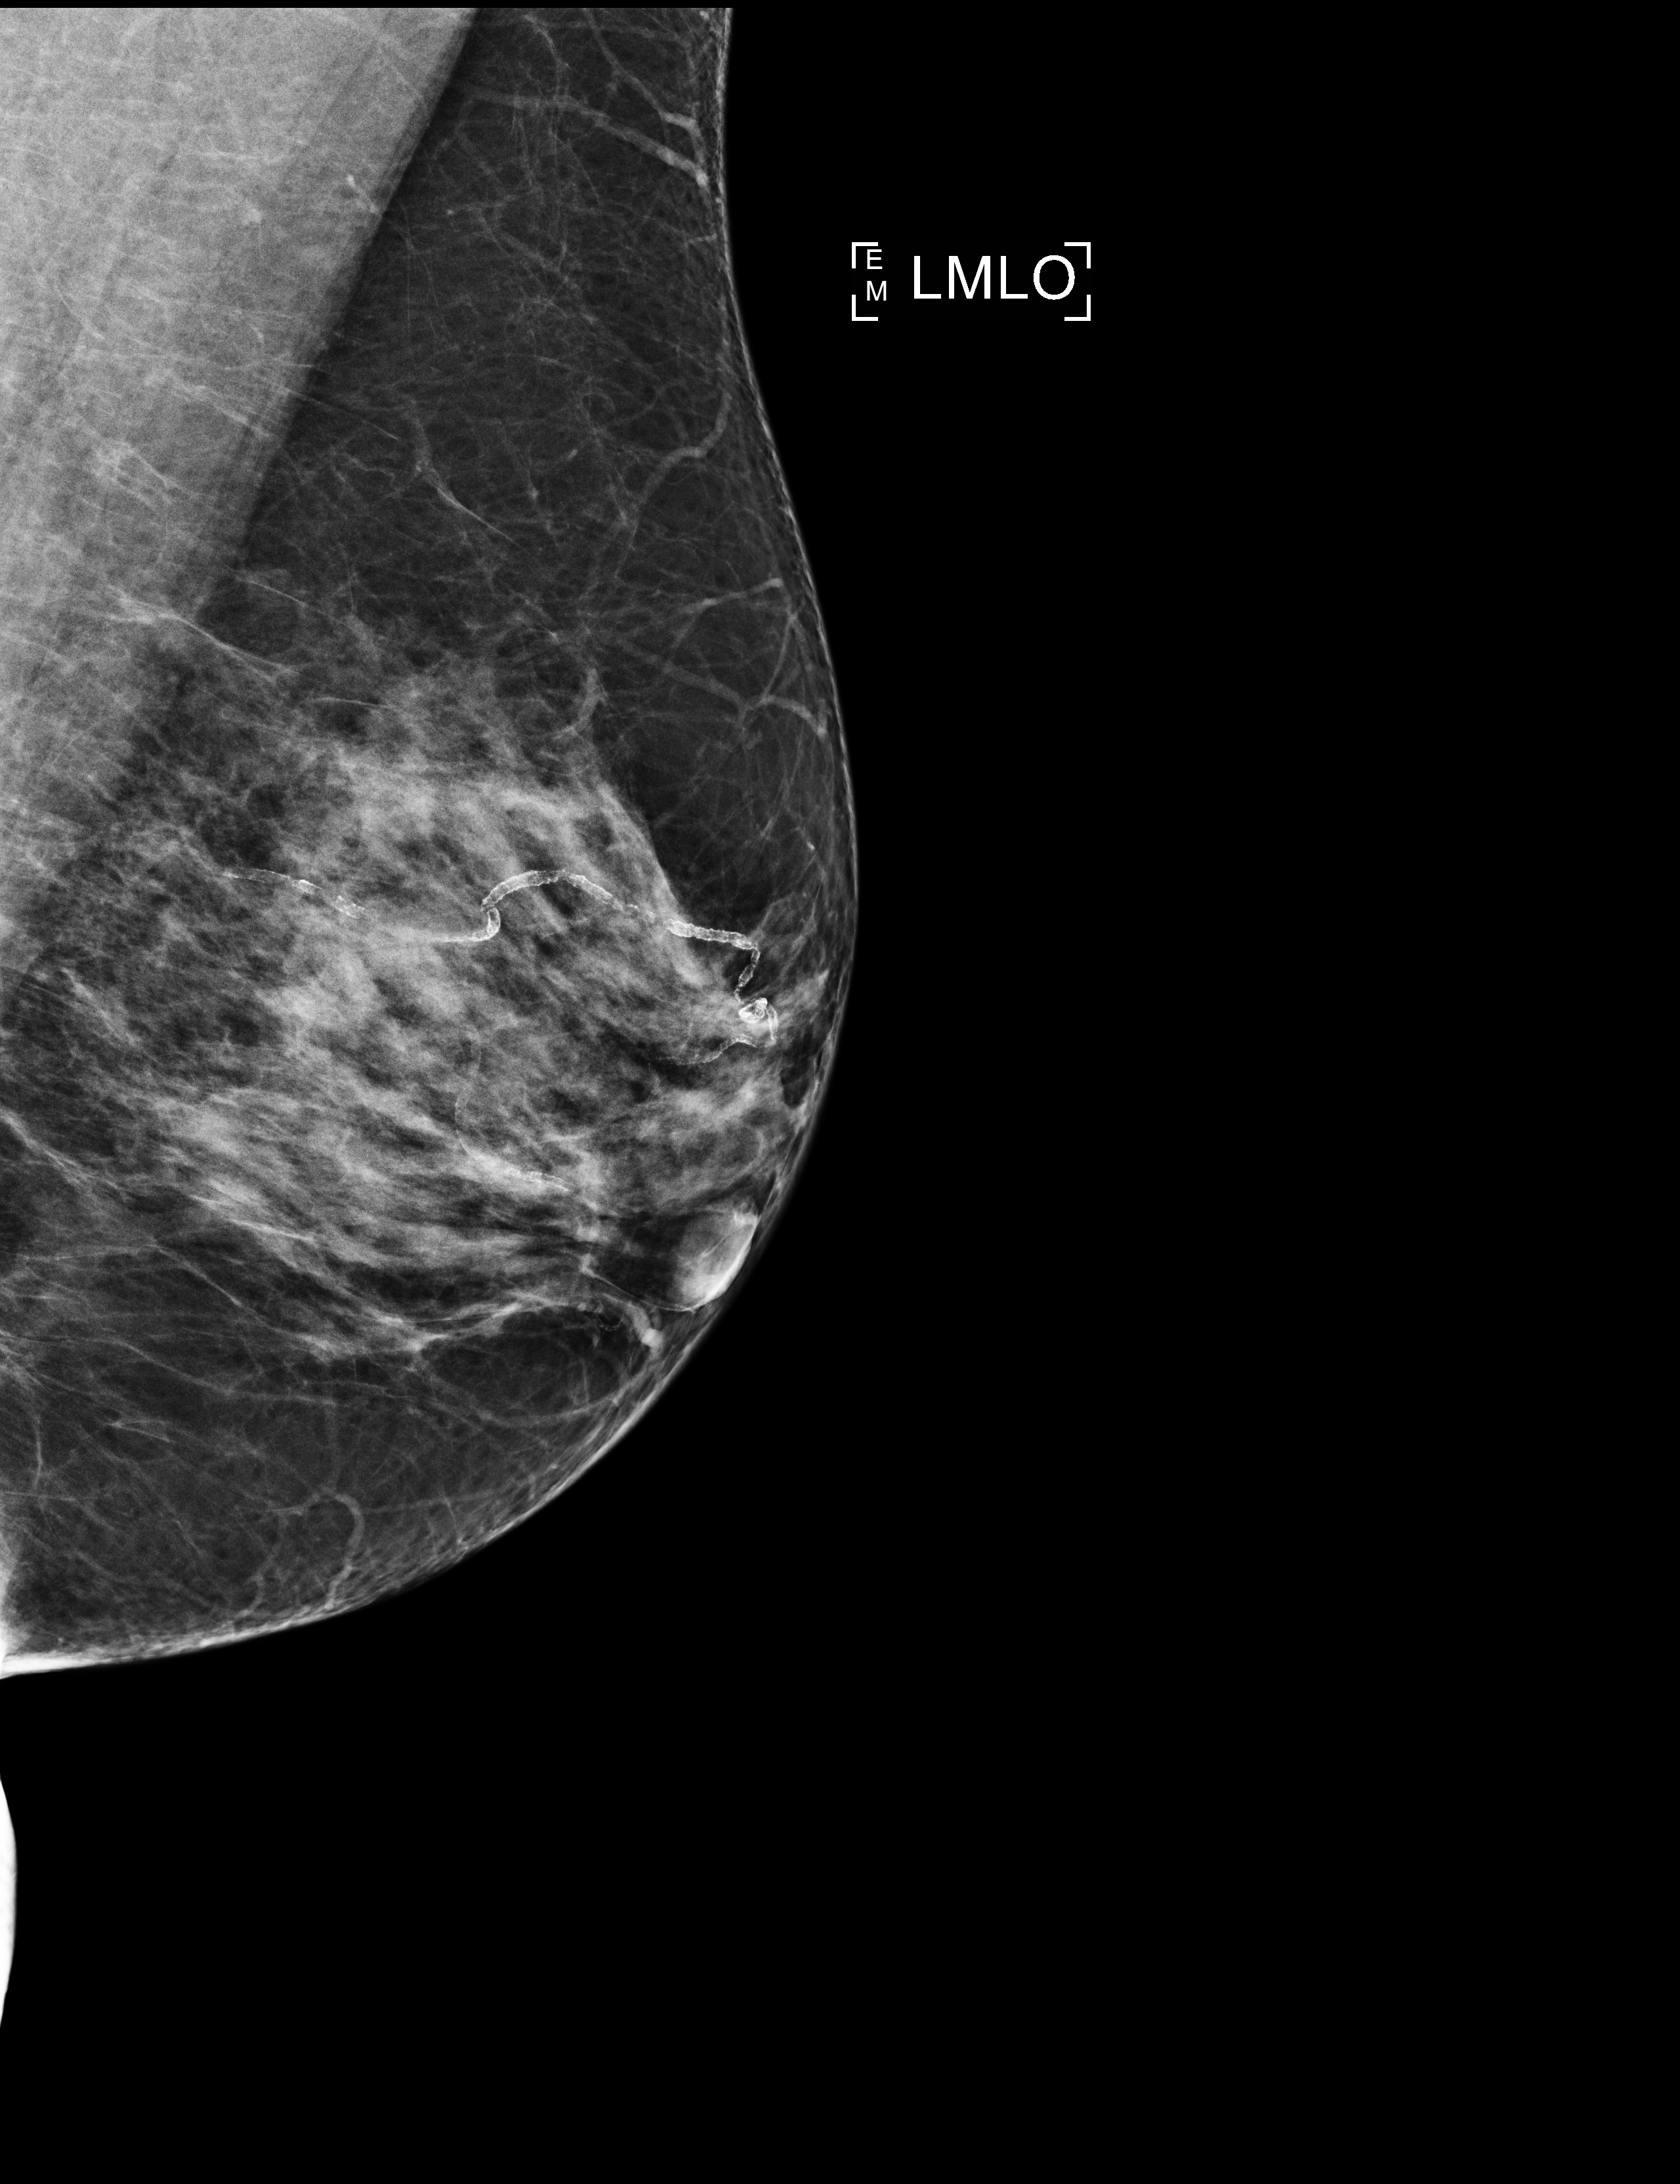
Digital mammogram (FFDM); left breast; MLO view; annual screening mammography examination; compressed breast thickness 60 mm. Female patient, age 59 years.
Final BI-RADS category for the screening round (tomosynthesis exam, both breasts): category 1.